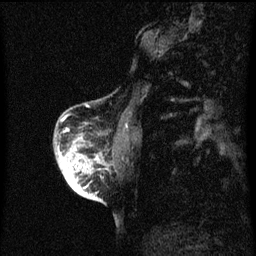
Breast MRI (dynamic contrast-enhanced), one sagittal slice. Dynamic contrast-enhanced series, image 2 of 3 at this slice position (ordered by acquisition). 1.5 T. TE 4.2 ms, TR 8 ms. 2 mm slice thickness. 256 × 256 image matrix, field of view 180 × 180 mm. Female patient, age 56 years.
Annotated regions visible in this slice (semi-automatic segmentation, software-assisted and operator-edited):
- analysis volume of interest (the breast-tissue region the enhancement analysis was run in; not a lesion): bounding box [x1, y1, x2, y2] px = [54, 122, 109, 199]
- tumour enhancement mask (voxels above the 70 % enhancement threshold inside the analysis volume of interest): [57, 146, 100, 197]